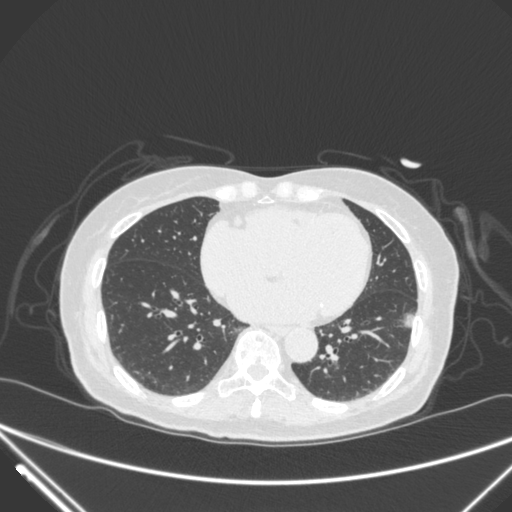
Chest CT, one axial slice; slice 117 of 310 in the series (ordered by position); 120 kVp; lung window (W 1500 / L -600 HU); 512 × 512 image matrix. Female patient, age 82 years. From the clinical record (not read from this slice): clinical TNM (as recorded): T1c N0 M0; histopathological grade: G2.
Annotated regions visible in this slice (bounding box drawn by a radiologist):
- lung tumour (recorded histology: adenocarcinoma): bounding box (x1, y1, x2, y2) in pixels: (389, 304, 419, 335)